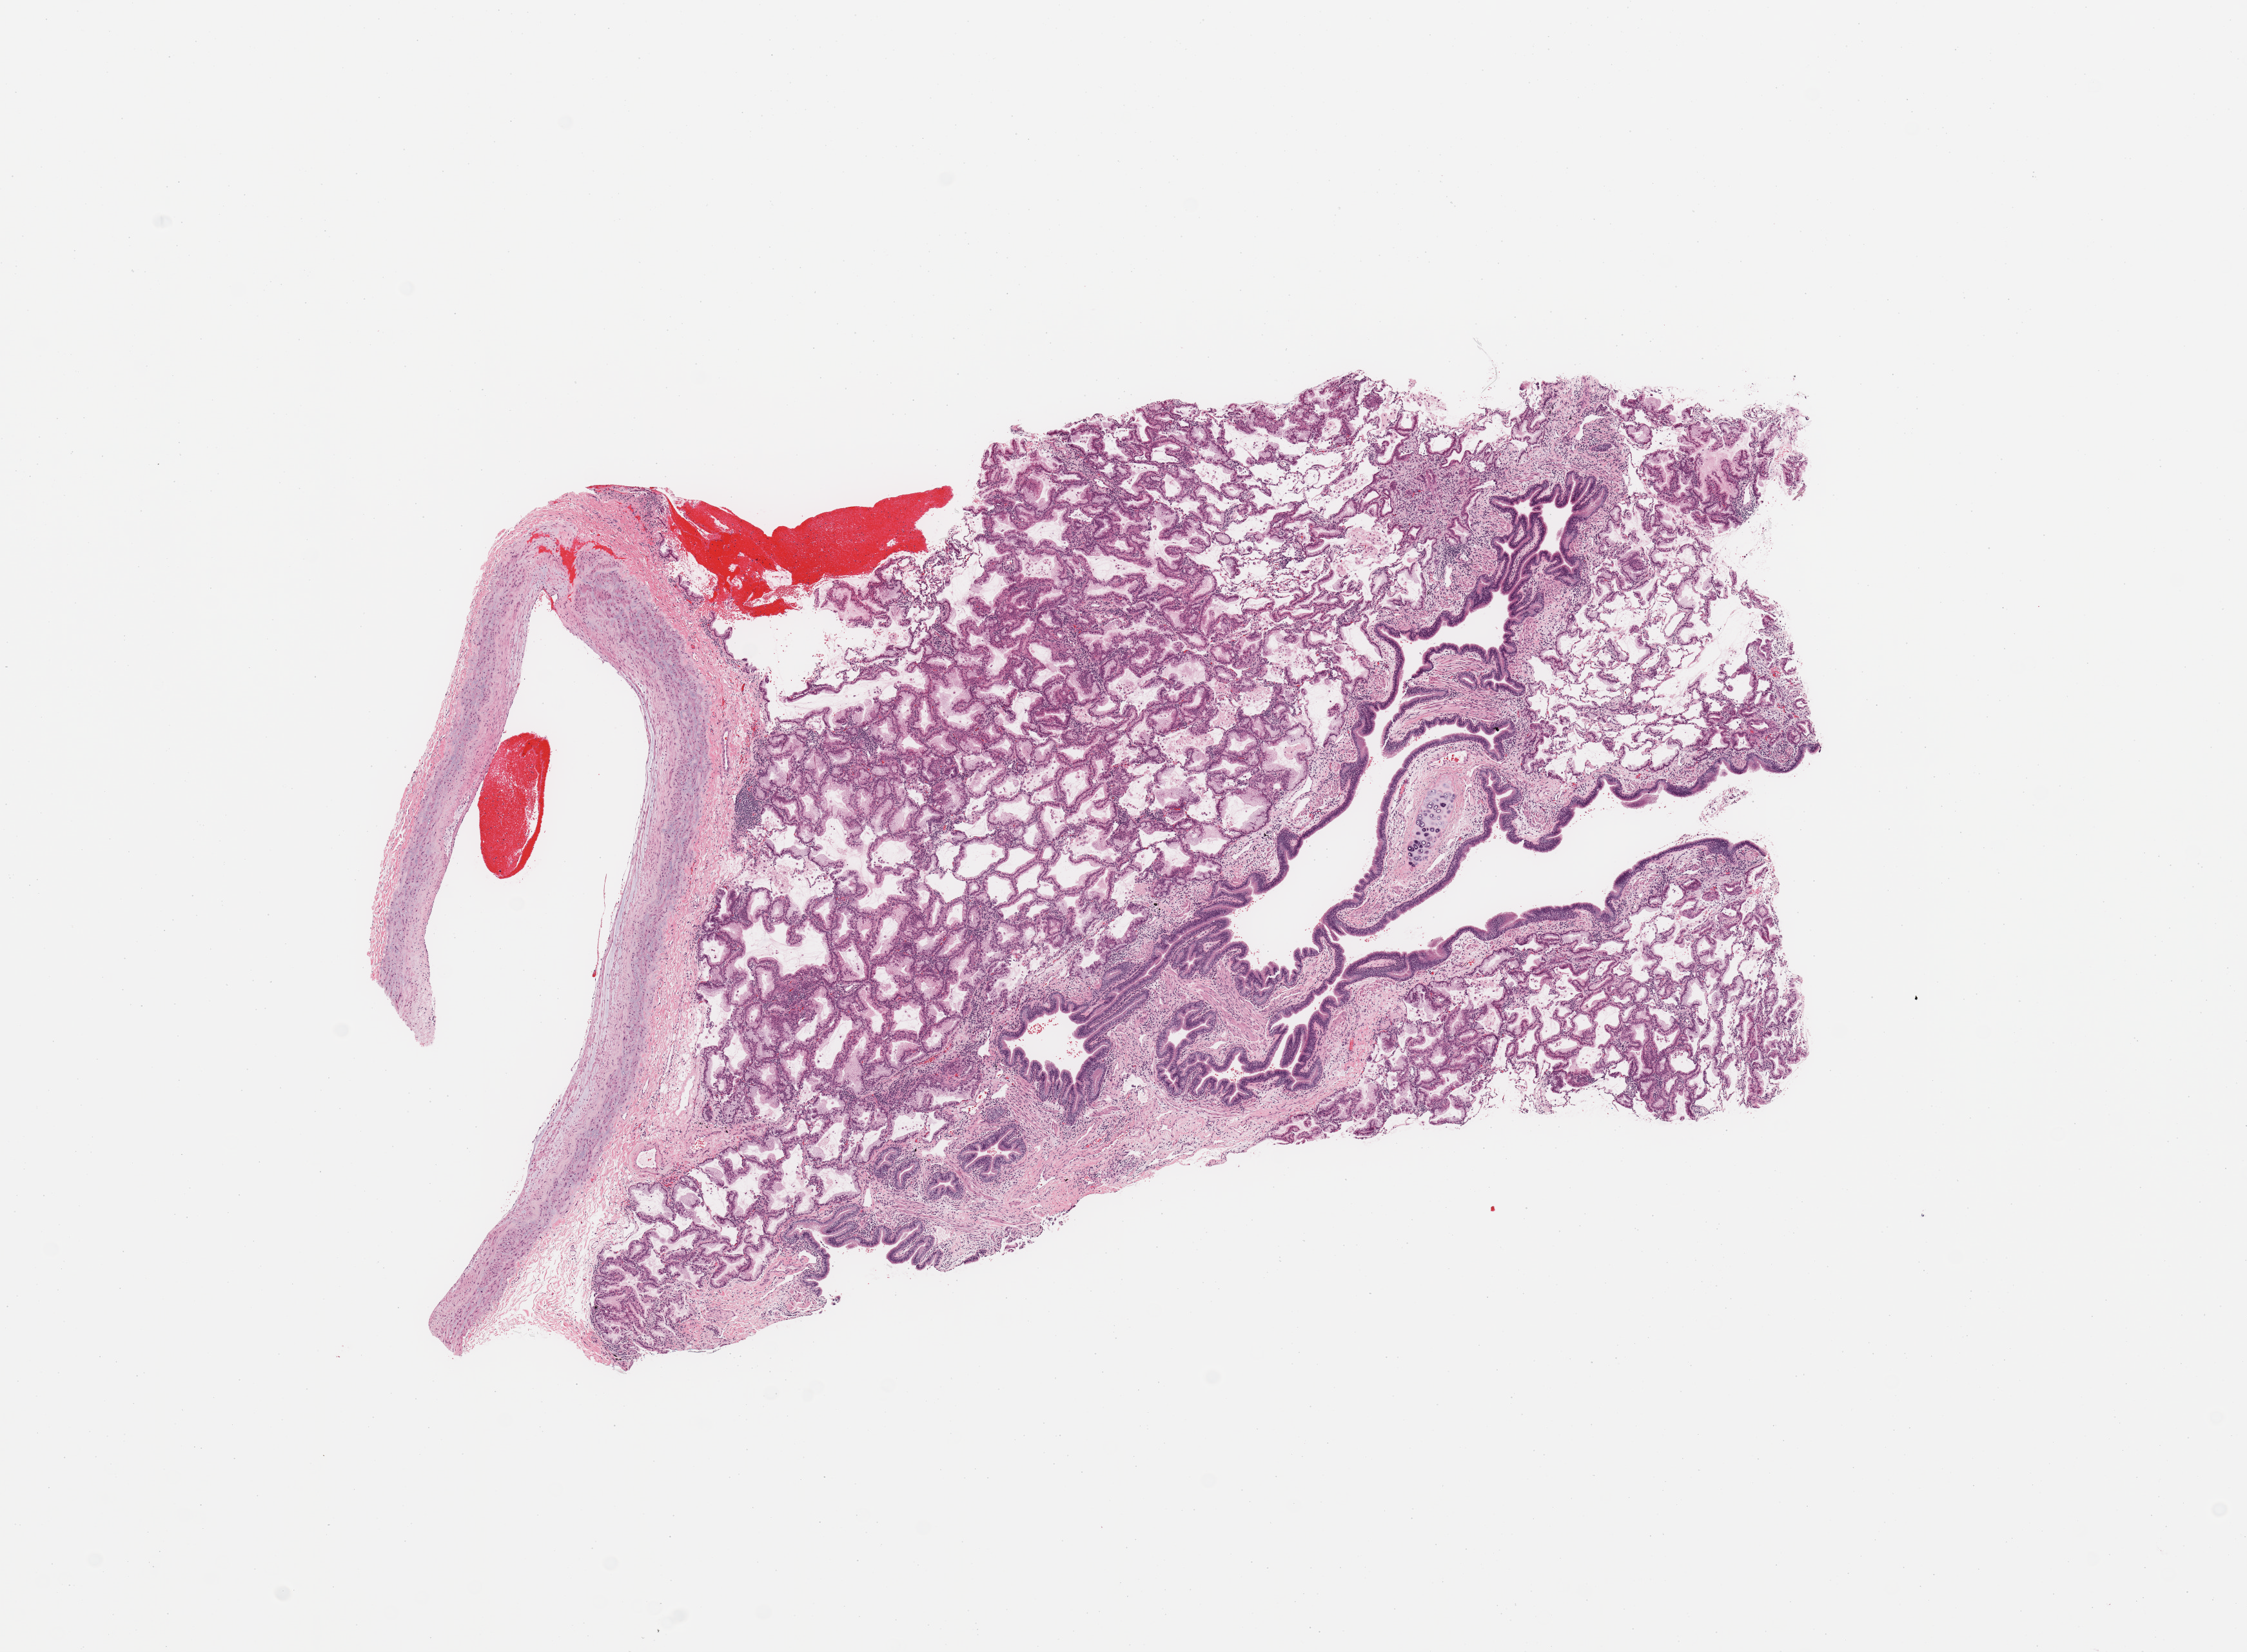
Digitized Hematoxylin and eosin (H&E) stained tissue section (whole slide), low-resolution overview of the scanned area, about 13.8 x 10.1 mm (slide scanned at 20x). Lung, tumour tissue. Patient: male, age 69 years. Histologic grade: G1 (well differentiated).
Primary tumour site (as recorded): left lower lobe. AJCC pathologic stage: IIB. Histologic diagnosis: Adenocarcinoma, NOS.